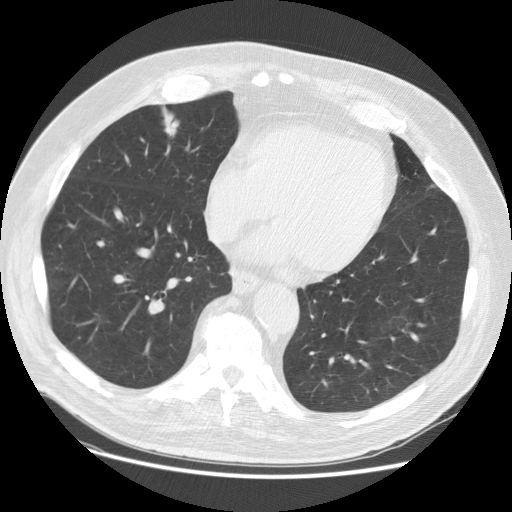
Low-dose screening chest CT, axial slice, baseline annual screen, lung window (W 1500 / L -600 HU), 2.5 mm slice thickness, slice 88 of 129 in the series. Male participant, aged 74 years at enrolment. Former smoker at enrolment.
Expert-annotated lung lesion, bounding box (x1, y1, x2, y2) in pixels: (148, 94, 187, 146). Screening reader's record for this exam (one nodule recorded; not confirmed to be the boxed lesion): non-calcified nodule or mass ≥4 mm, right middle lobe, 24 × 24 mm, spiculated (stellate) margins, soft tissue attenuation. Official screen result: positive, change unspecified: nodule(s) >= 4 mm or enlarging nodule(s), mass(es), or other non-specific abnormalities suspicious for lung cancer. Lung cancer was diagnosed 296 days after this screen: papillary adenocarcinoma, NOS, right middle lobe, well differentiated (G1), stage IA (AJCC 6th edition), 20 mm at pathology.